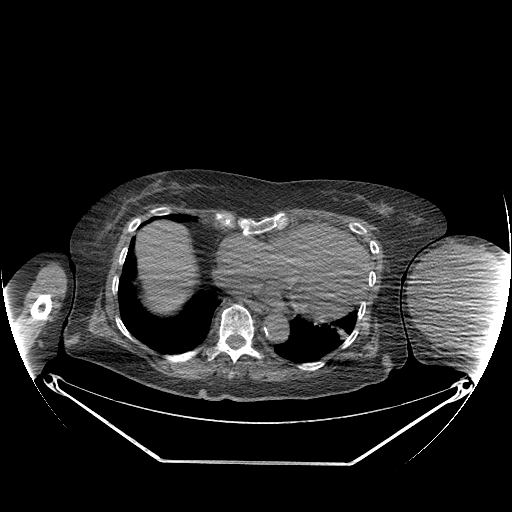
CT of an extremity soft-tissue mass (from a PET/CT study), one axial slice. Position 152 of 267 along the scan axis. Soft-tissue window (W 400 / L 40 HU). 3.75 mm slice thickness. 512 × 512 image matrix. Female patient. Case-level facts recorded for this patient, not image findings: histological type: pleiomorphic leiomyosarcoma; grade: high; site of the primary tumour: left biceps.
Annotated regions visible in this slice (expert contour drawn on MRI and transferred to this co-registered scan by the dataset authors):
- gross tumour volume including surrounding oedema: bounding box <411,246,499,328> (left, top, right, bottom; pixels)
- gross tumour volume (mass): <411,246,499,325>